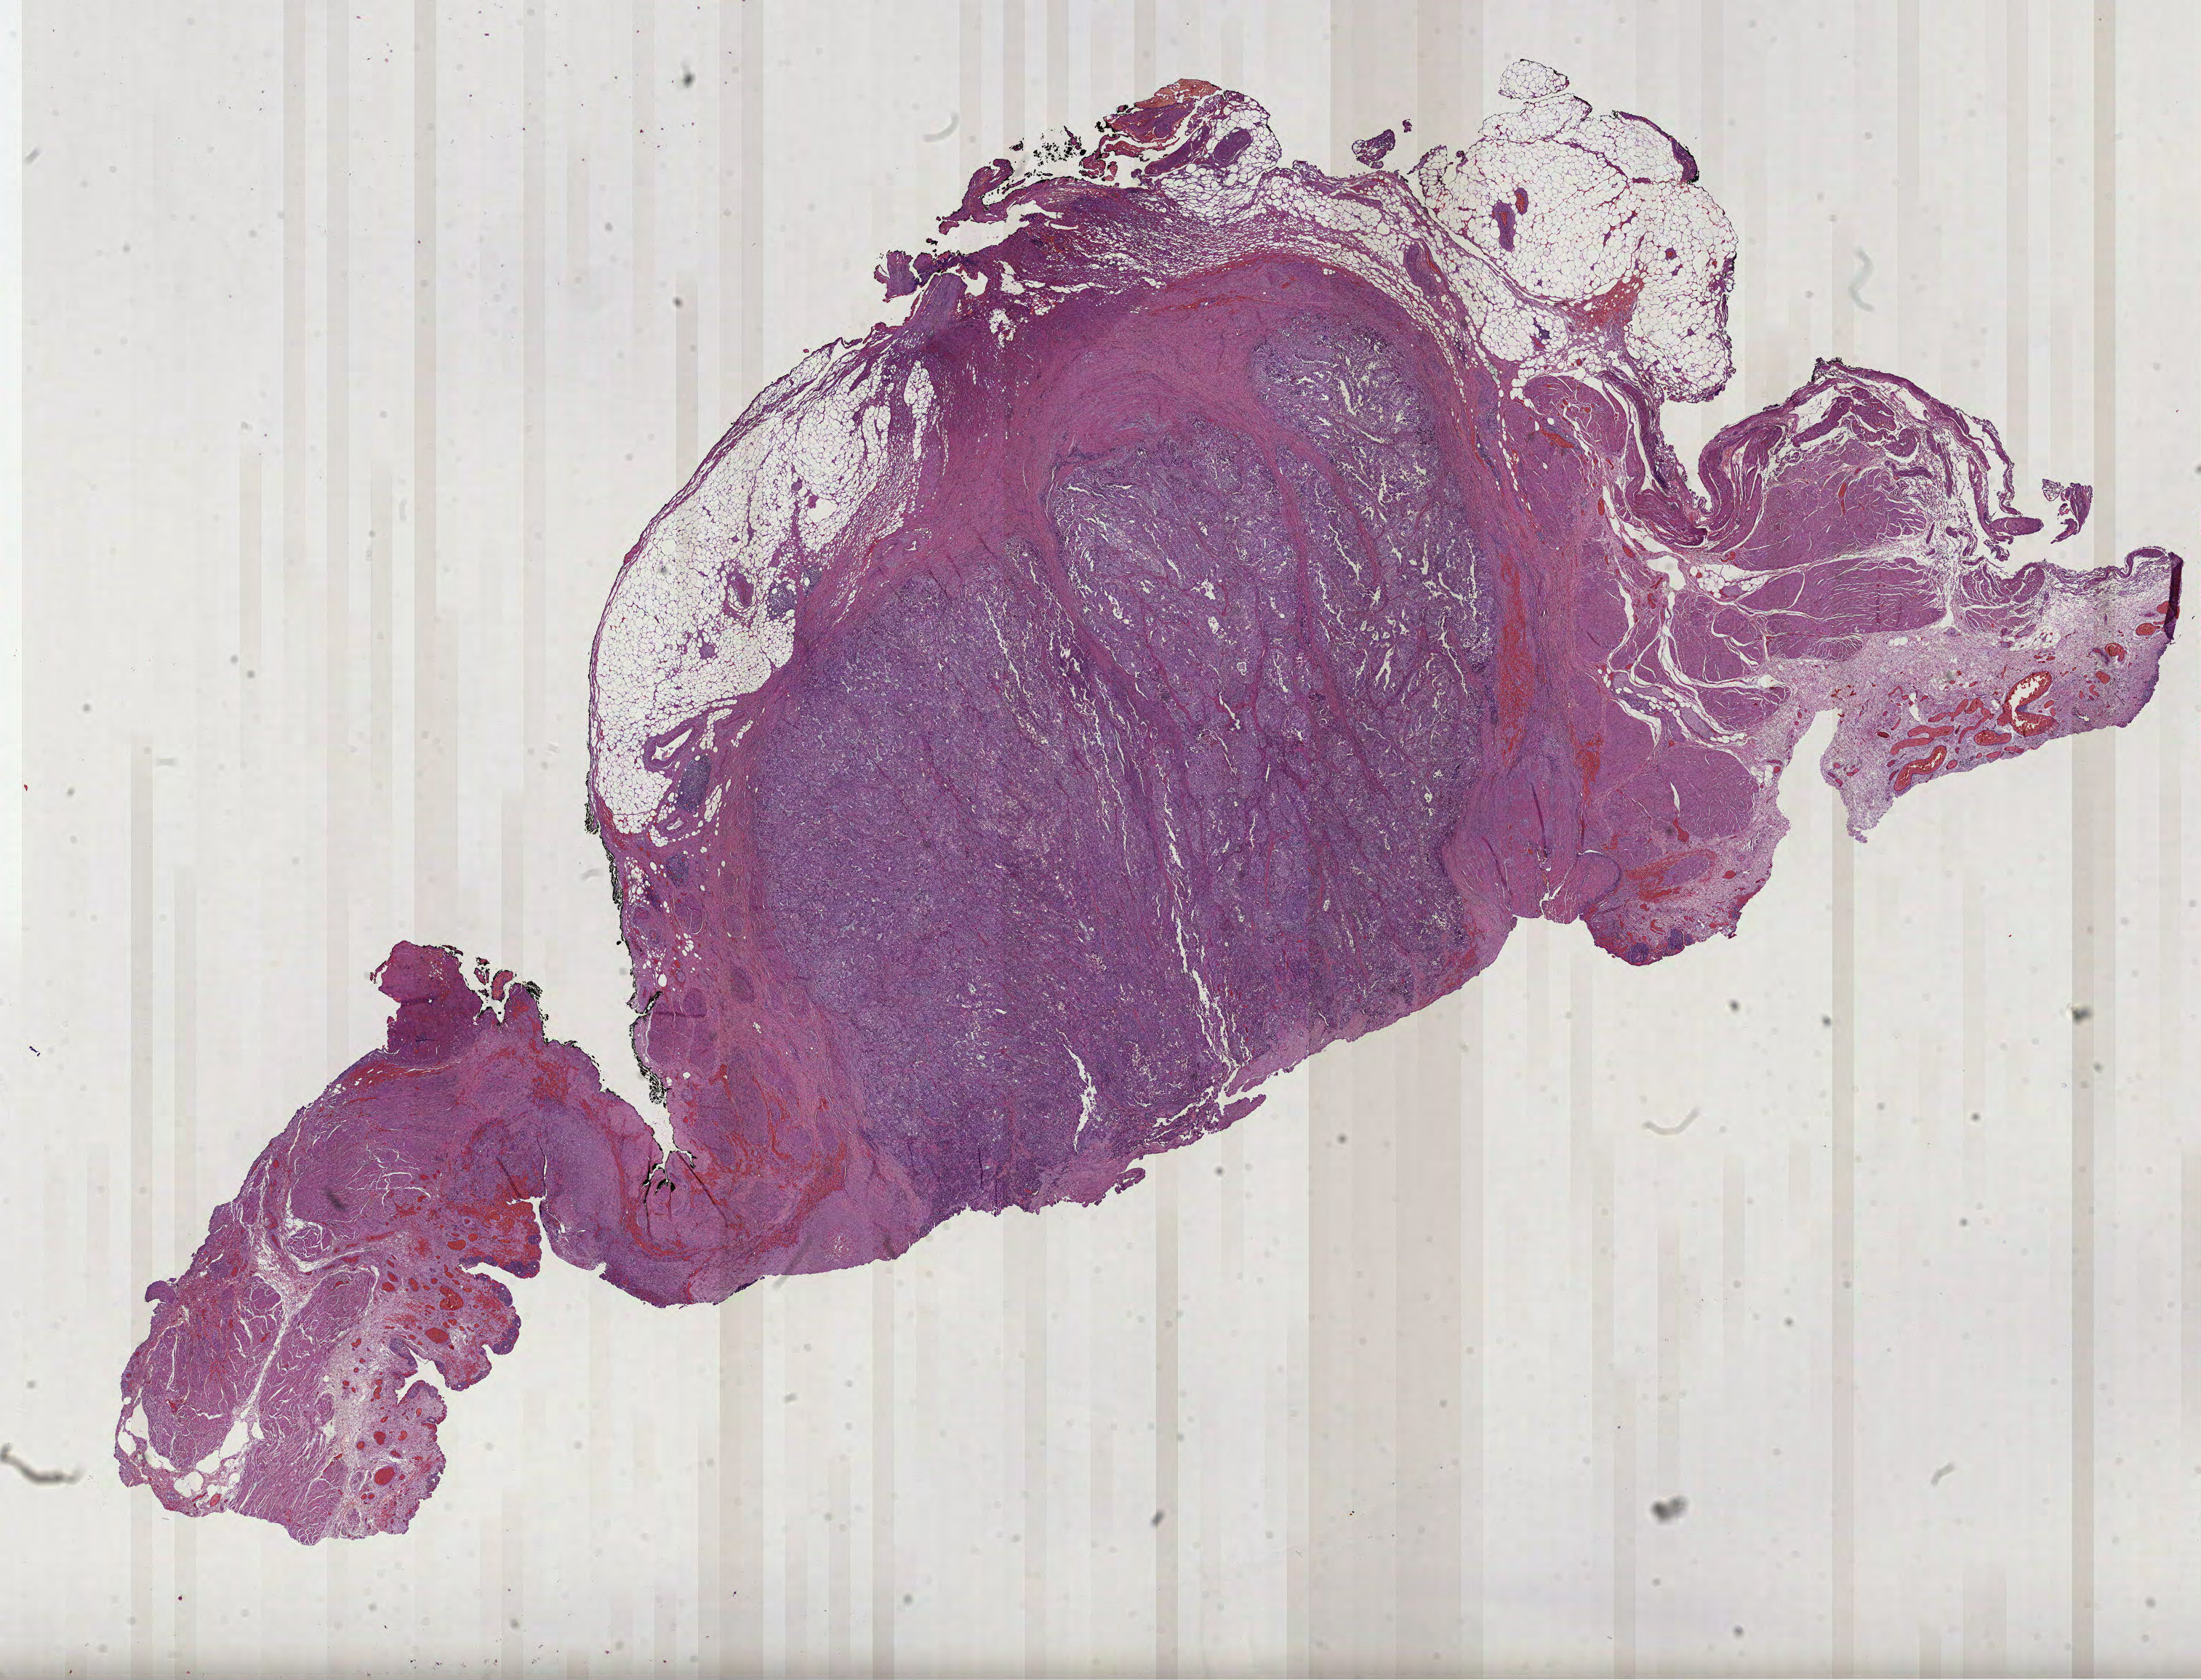
H&E-stained whole-slide image — a low-resolution overview of the entire scanned area, about 24.4 x 18.6 mm (from a 40x scan); formalin-fixed paraffin-embedded (FFPE) diagnostic section; primary tumour sample from the bladder. Female patient; age at initial diagnosis 83 years. Histologic grade: high grade.
AJCC pathologic stage: III. Pathologic diagnosis: Transitional cell carcinoma (trigone of bladder). TNM: T3a N0 M0.